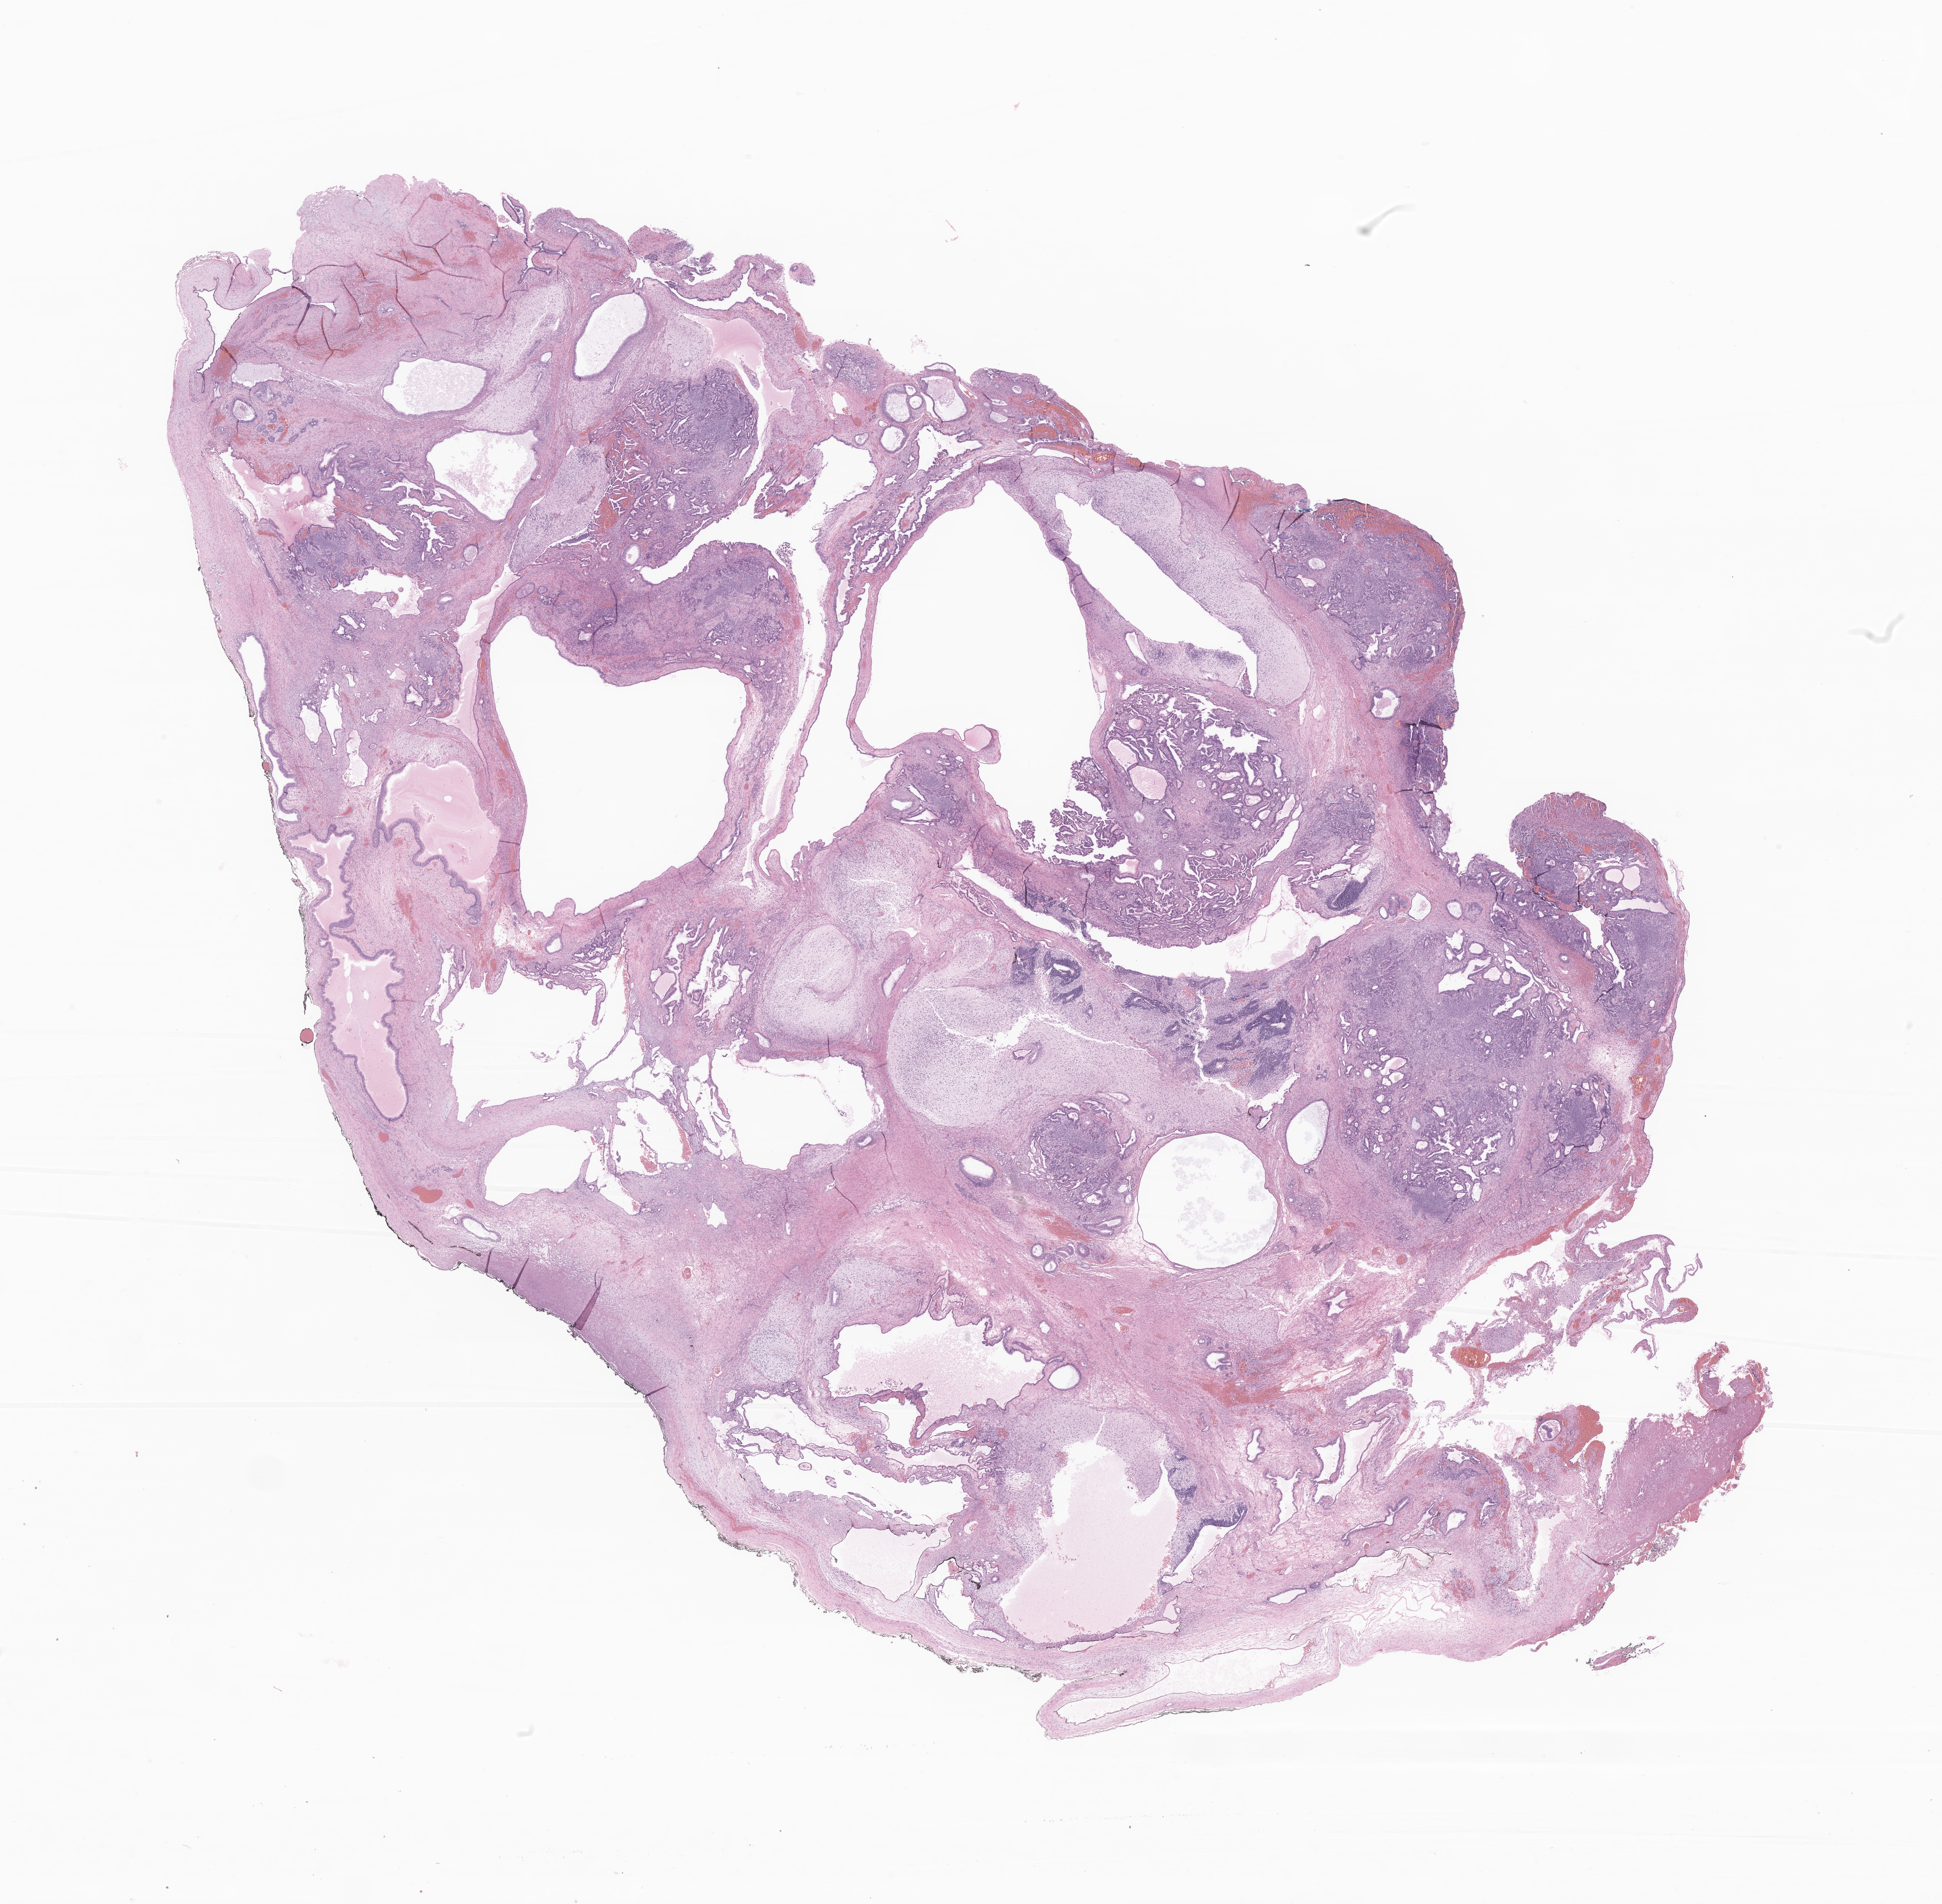
Whole-slide image, haematoxylin and eosin stain of tumor tissue from the brain — whole scanned area (about 22.1 x 21.6 mm) shown as a low-resolution overview. Formalin-fixed, paraffin-embedded (FFPE) tissue. Male patient, age 82 months (6 years 10 months).
Diagnosis (ICD-O-3 morphology term): Glioma, malignant.